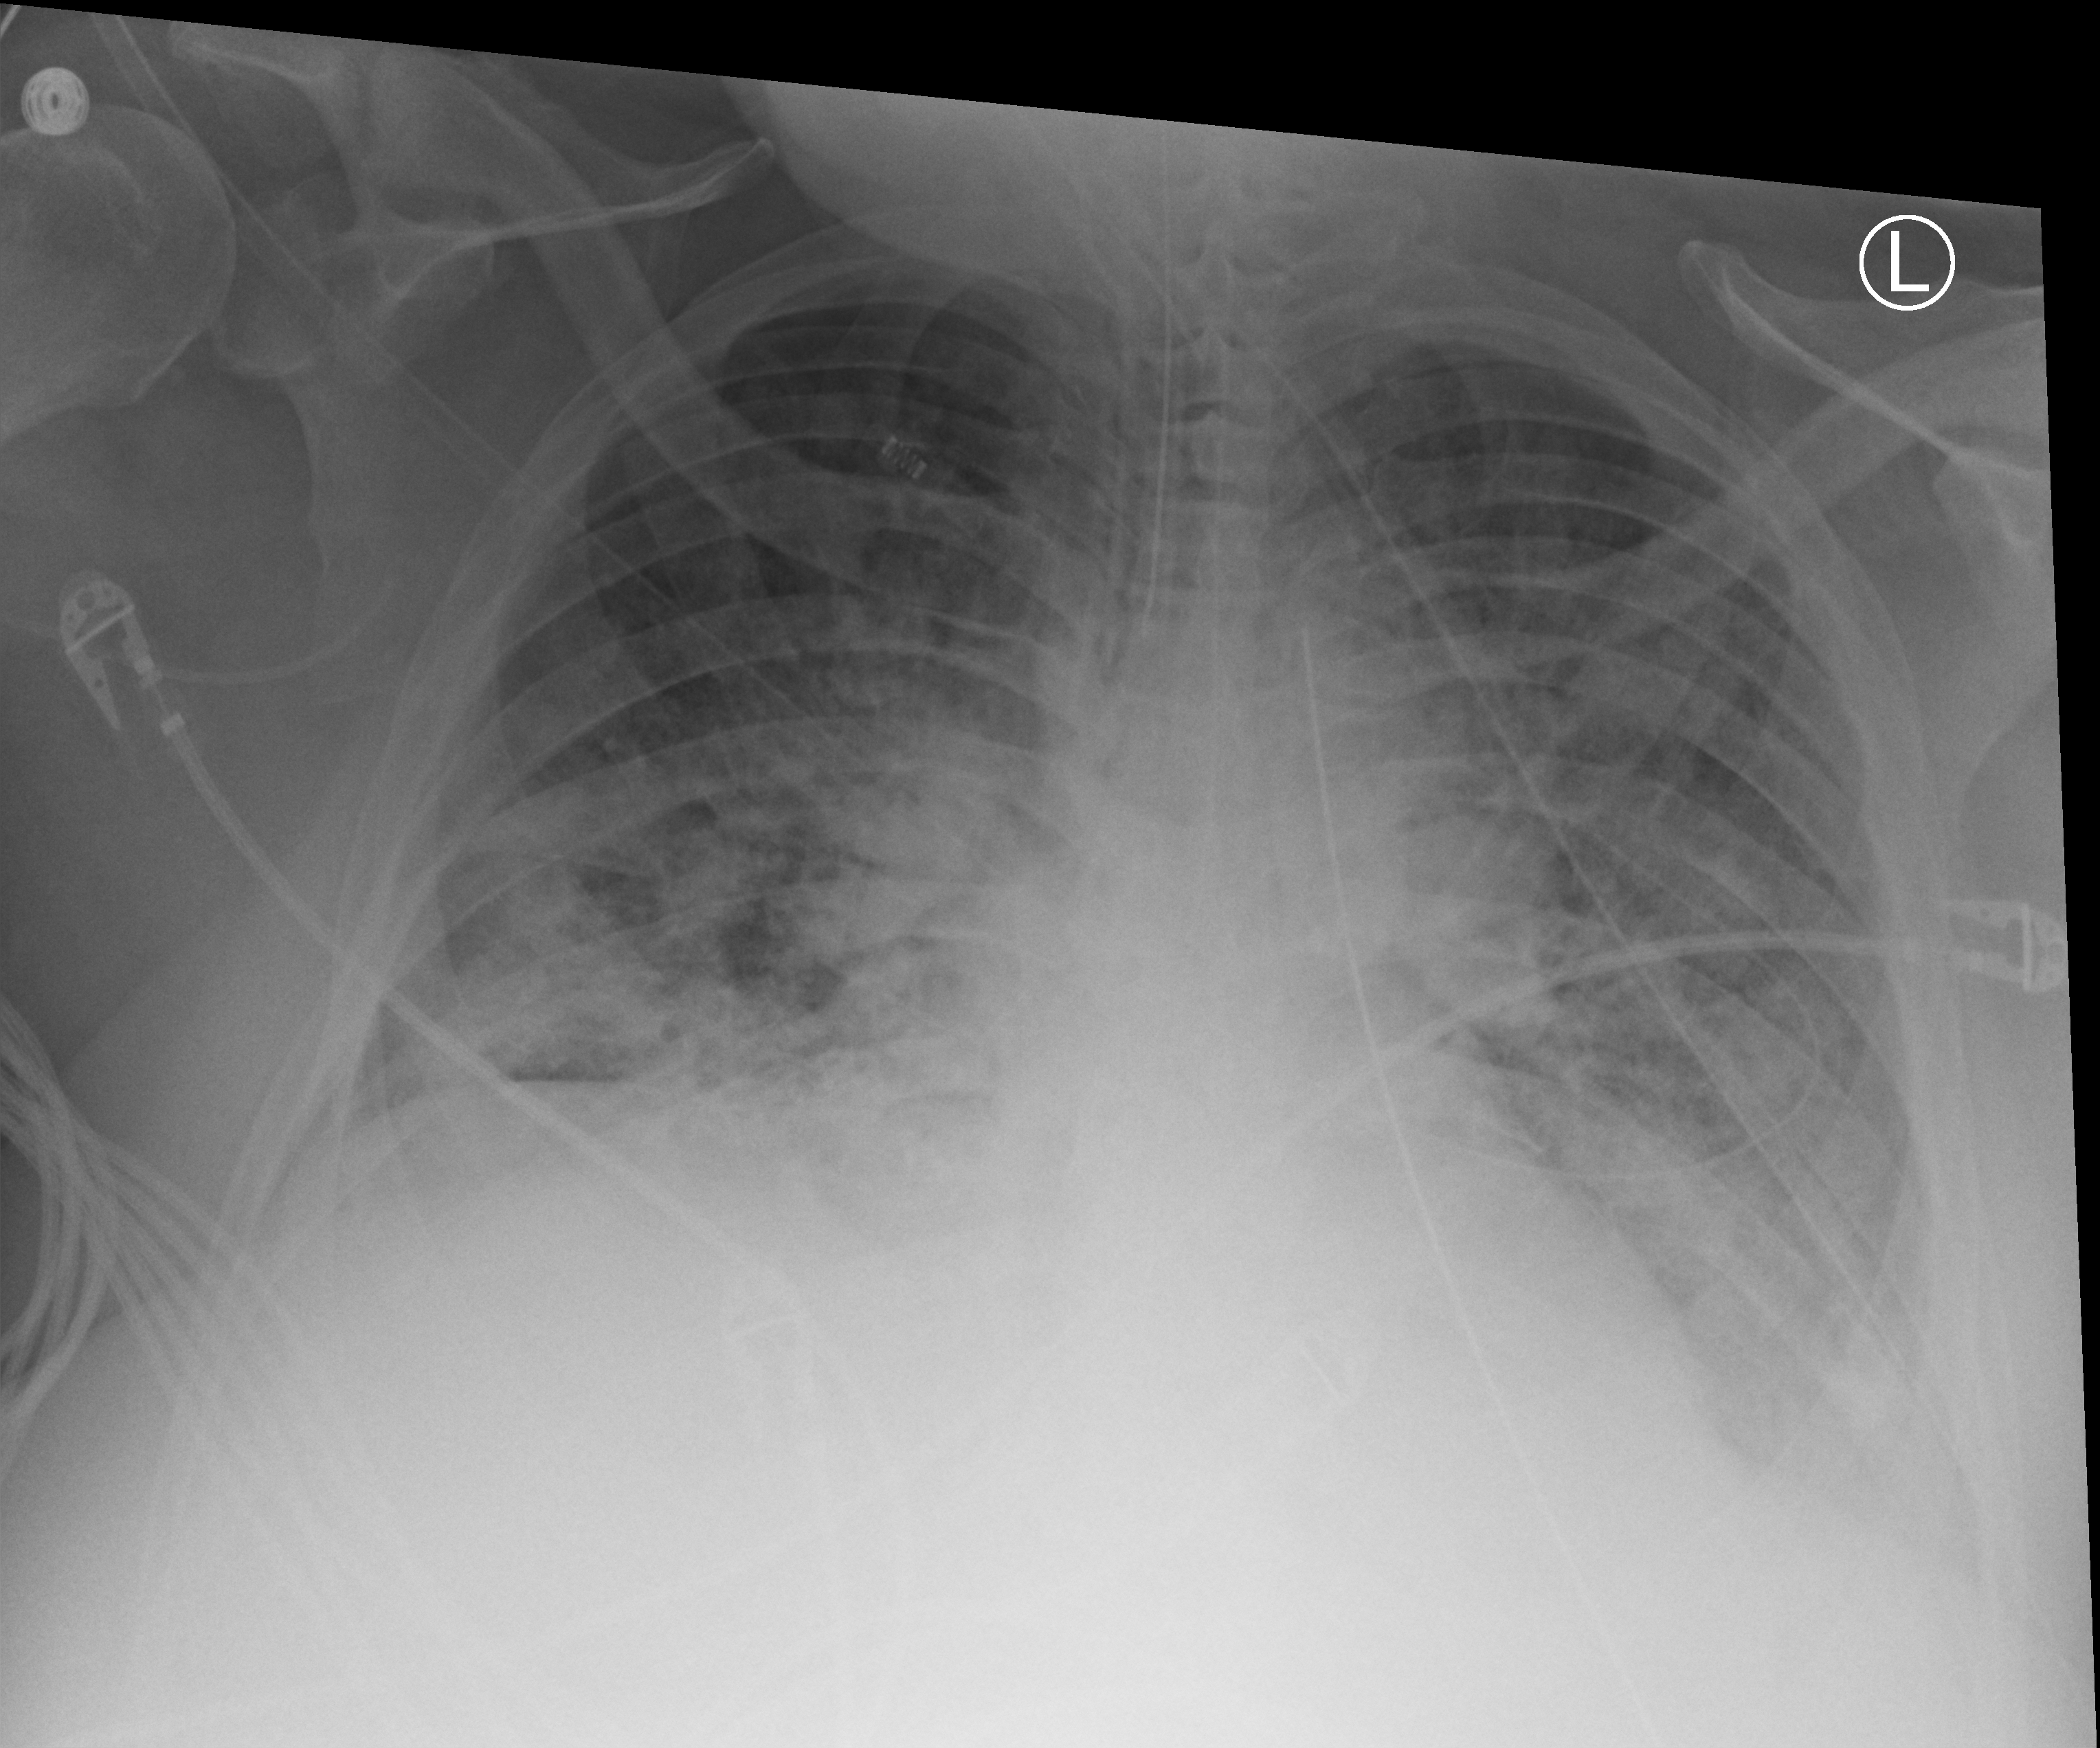
Bedside chest radiograph (computed radiography); anteroposterior (AP) projection. Male patient hospitalised with COVID-19, age 60–74 years.
Admission-level facts for this patient (not findings on this image; timing relative to this image not recorded): smoking status (admission record): never; hypertension (admission record): yes.